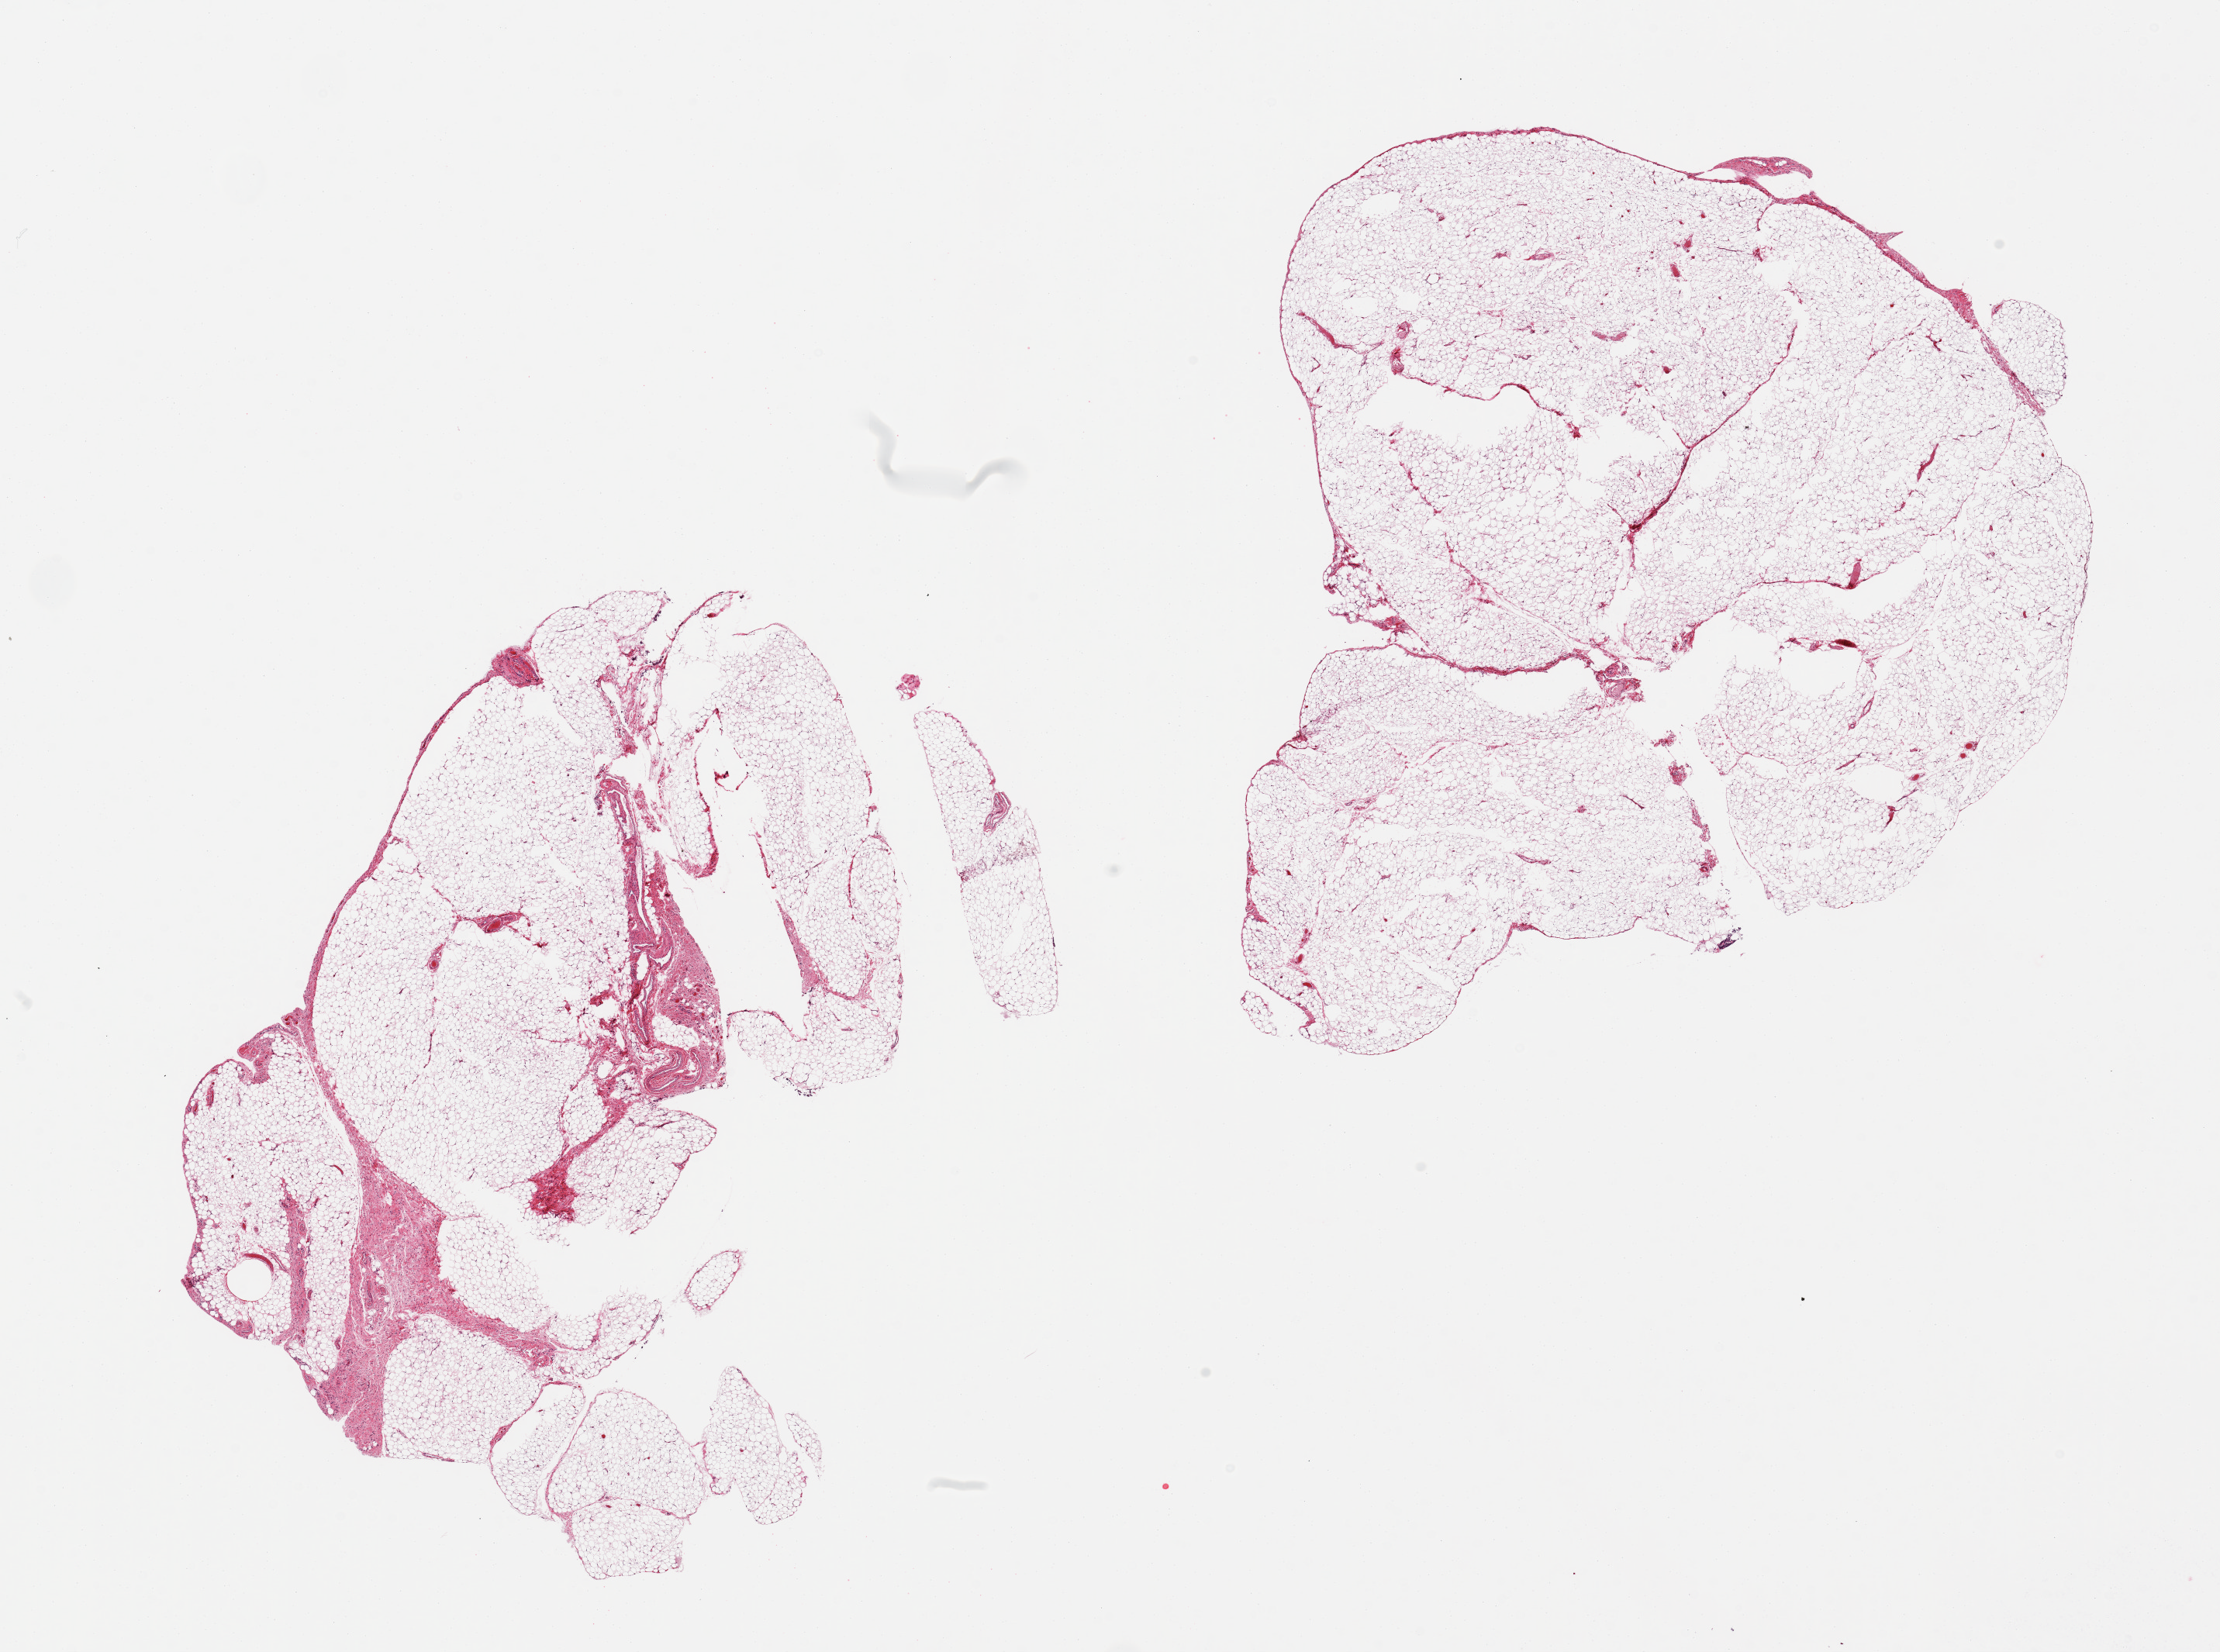
Hematoxylin and eosin (H&E) whole-slide image, brightfield — whole scanned area (about 22.6 x 16.9 mm, acquisition: 20x scan) shown as a low-resolution overview; PAXgene-fixed, paraffin-embedded tissue; sampled site (target tissue): omentum; donor tissue sample. Donor sex: male.
Pathologist's review note for this sample: 2 pieces; 10% fibrous content in 1 piece; minimal in the other.